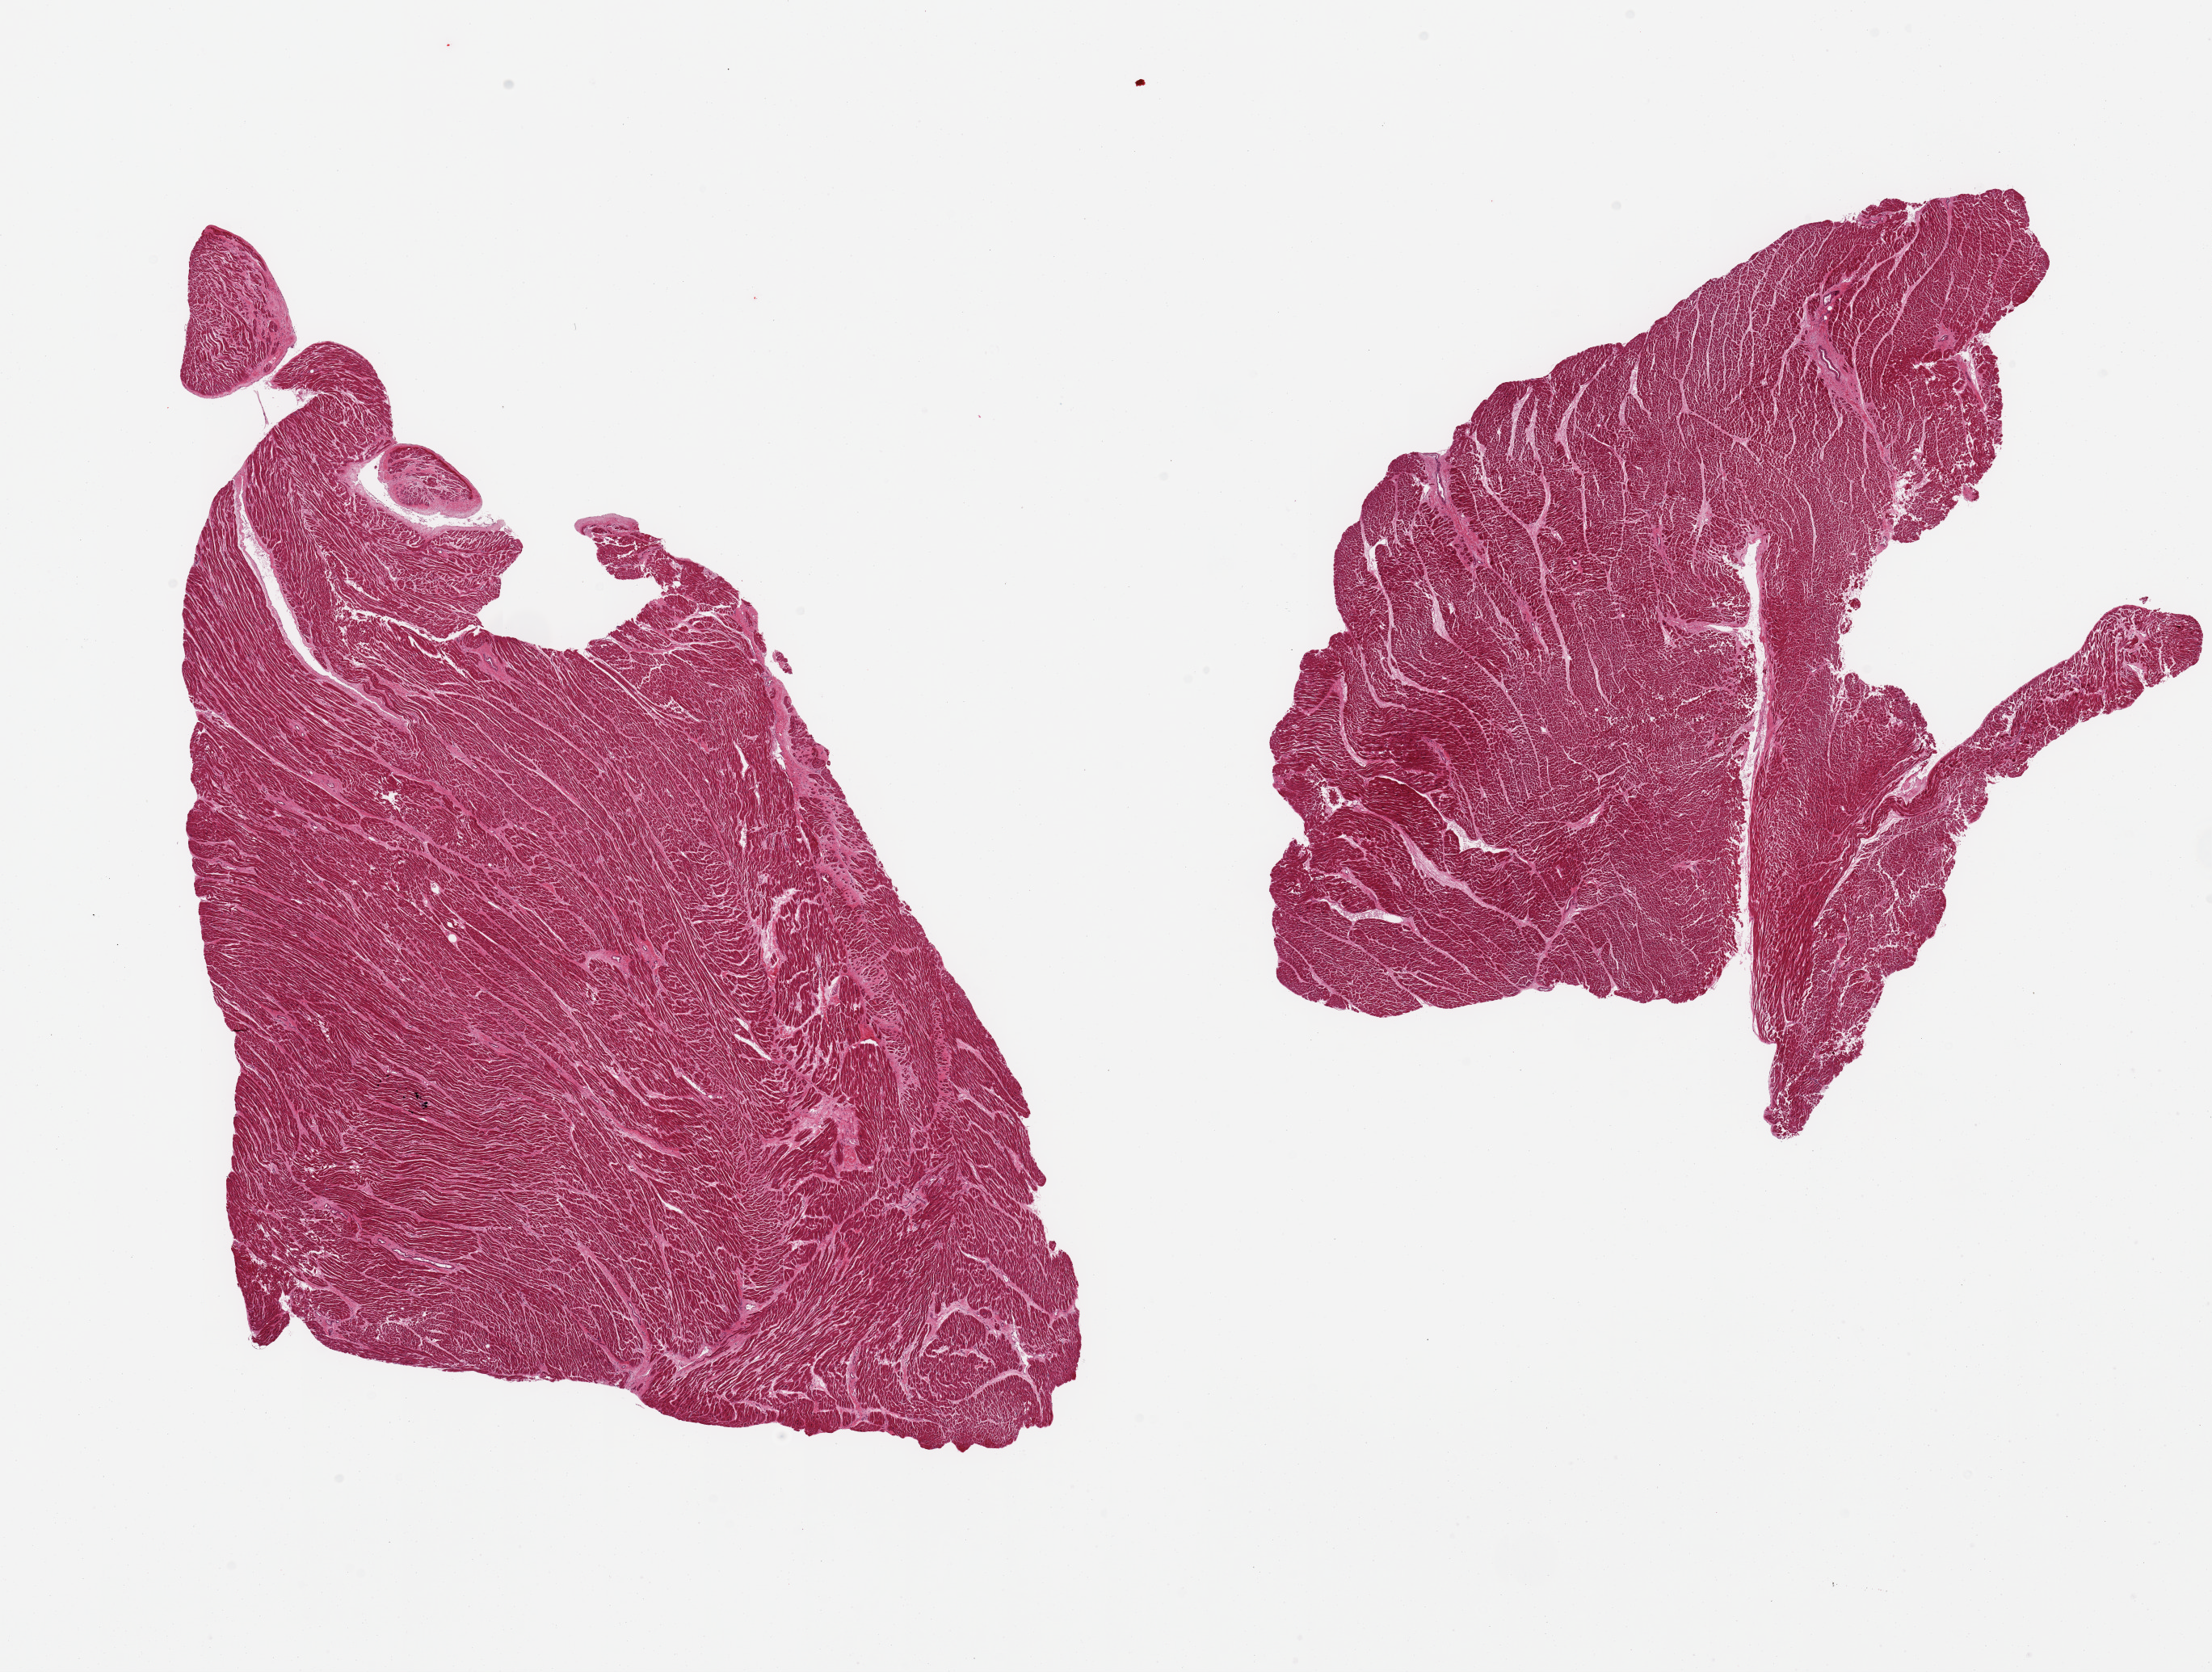
Whole-slide image, hematoxylin and eosin (H&E) stain, brightfield — whole scanned area (about 21.7 x 16.4 mm) shown as a low-resolution overview. PAXgene-fixed, paraffin-embedded tissue. Sampled site (target tissue): heart. Tissue donor sample. Donor: female.
Reviewer comment on this tissue sample: 2 pieces.